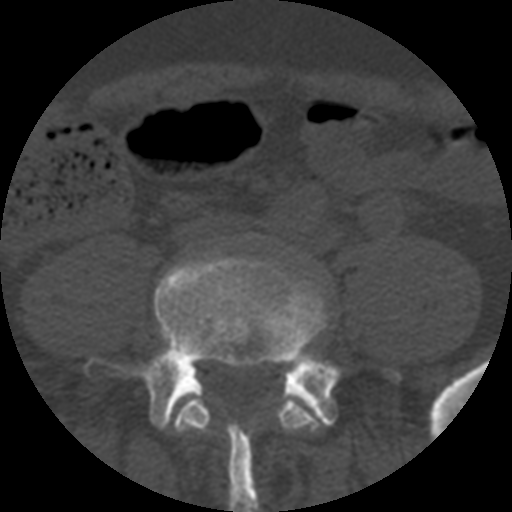
CT including the spine, one axial slice; slice 73 of 508 in the series (ordered by position); reconstruction kernel STANDARD; bone window (W 1800 / L 400 HU); 512 × 512 image matrix. Patient age 57 years. Case-level facts recorded for this patient, not image findings: primary cancer: prostate.
Structures marked on this image (semi-automatic segmentation, software-assisted and operator-edited):
- L4 vertebra: bounding box [x1, y1, x2, y2] px = [174, 391, 326, 433]
- L5 vertebra: [86, 255, 338, 512]